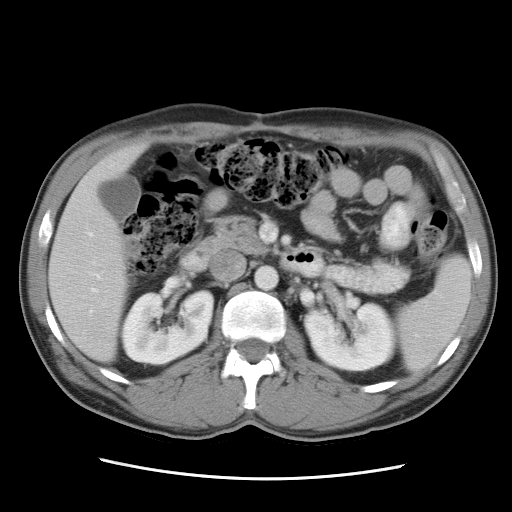
Contrast-enhanced abdominal CT, one axial slice; position 13 of 34 along the scan axis; reconstruction kernel STANDARD; intravenous contrast given; soft-tissue window (W 400 / L 40 HU); 7.5 mm slice thickness; 512 × 512 image matrix. Male patient, age 40 years. Case-level facts recorded for this patient, not image findings: diagnosis: colorectal cancer liver metastases, imaged before liver resection; multiple liver metastases: yes; largest metastasis: 1.5 cm; disease in both lobes: yes.
Structures marked on this image (outlined manually by an expert reader):
- liver: bounding box (x1, y1, x2, y2) in pixels: (49, 146, 145, 360)
- planned liver remnant (the part of the liver to remain after resection): (50, 146, 145, 360)
- portal vein (with intrahepatic branches): (88, 233, 100, 293)